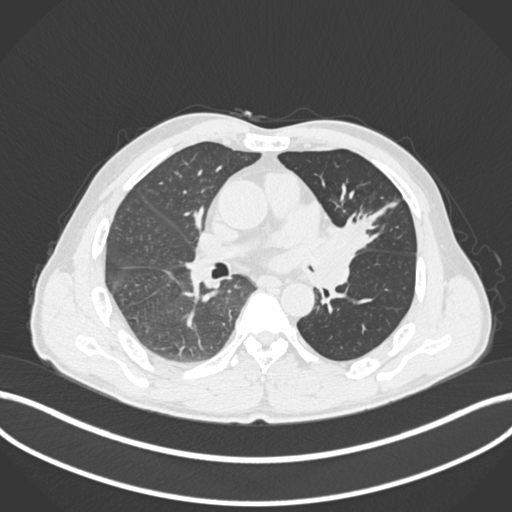
Chest CT, one axial slice; slice 99 of 255 in the series (ordered by position); reconstruction kernel B30f; 120 kVp; lung window (W 1500 / L -600 HU); 1 mm slice thickness; 512 × 512 image matrix, field of view 400 × 400 mm. Male patient, age 57 years. Case-level facts recorded for this patient, not image findings: clinical TNM (as recorded): T2b N0 M0.
Annotated regions visible in this slice (bounding box drawn by a radiologist):
- lung tumour (recorded histology: squamous cell carcinoma): bounding box (x1, y1, x2, y2) in pixels: (315, 211, 373, 259)